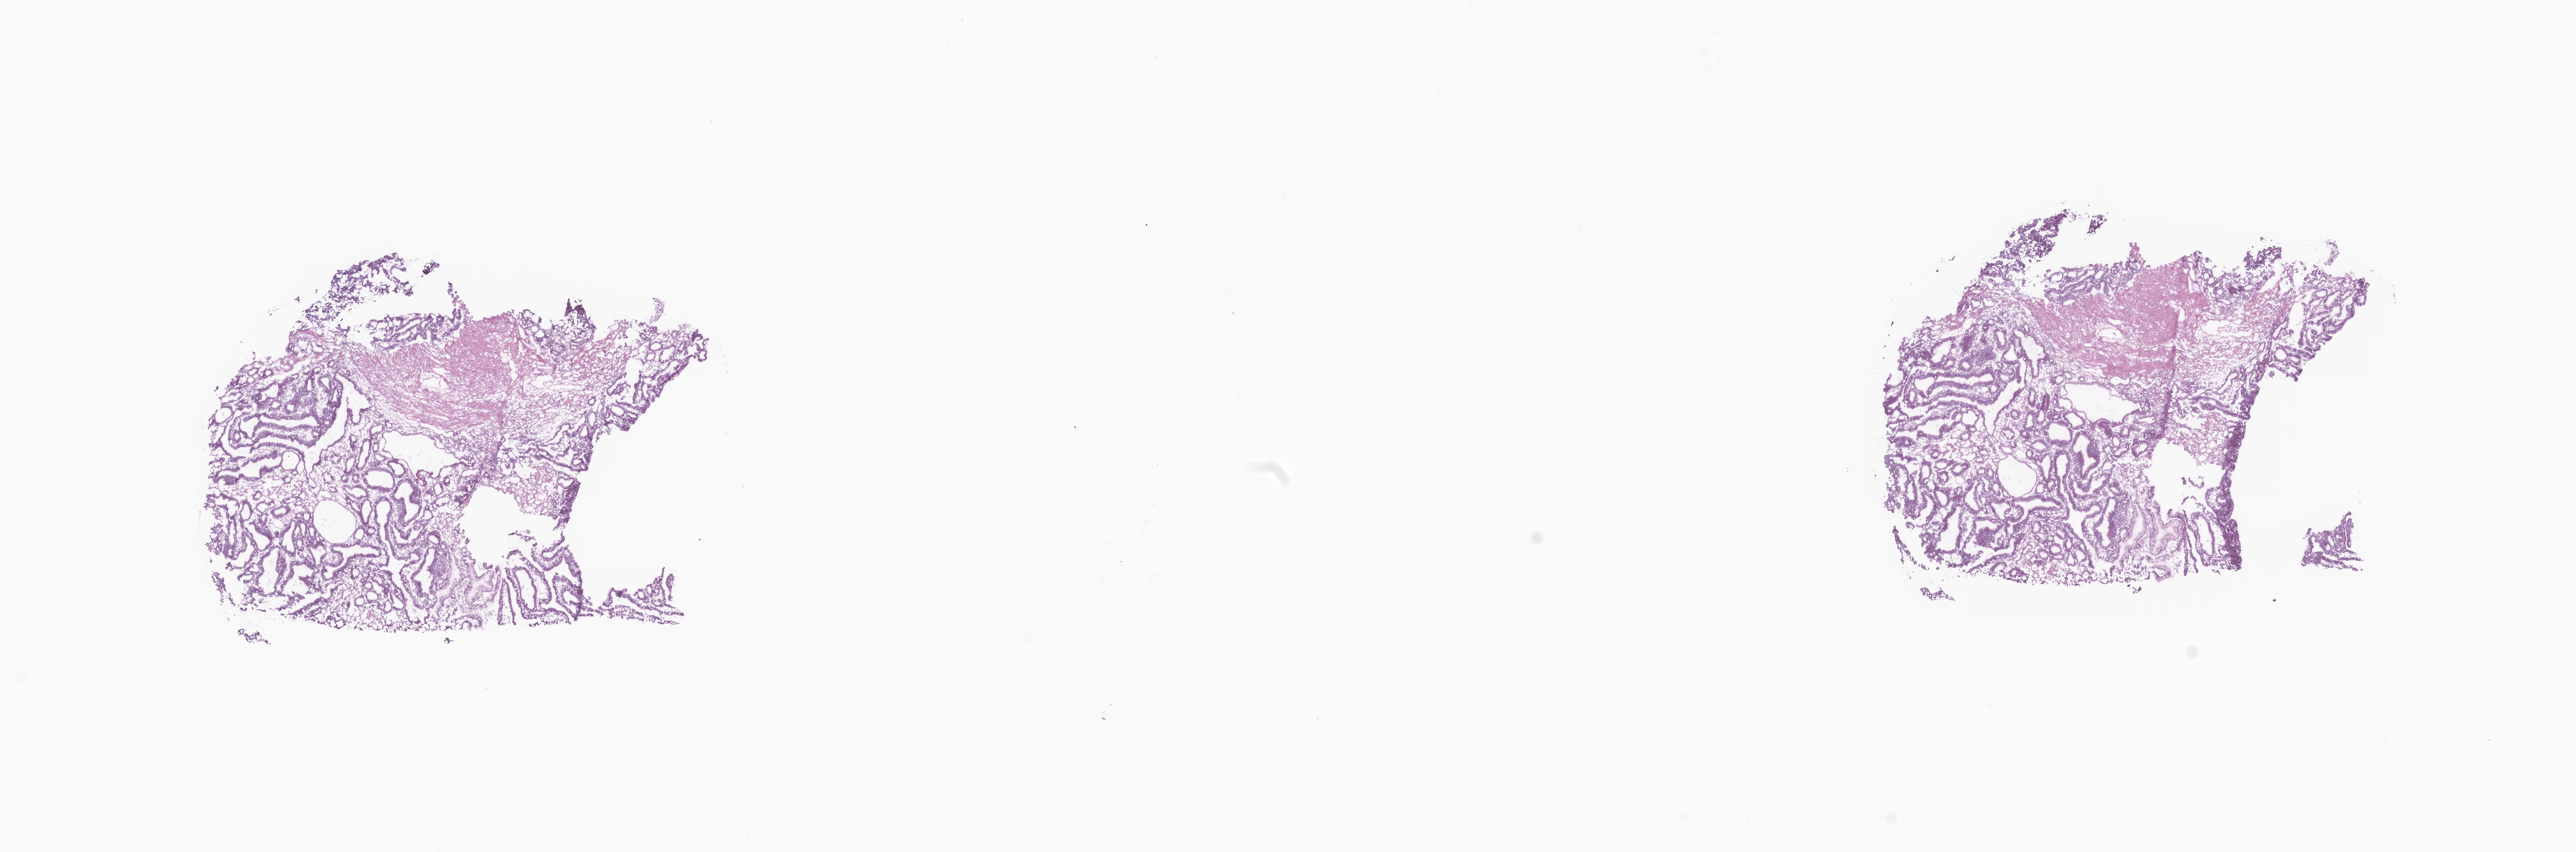
Whole-slide image, hematoxylin and eosin (H&E) stain, whole scanned area (about 23.2 x 7.7 mm) shown as a low-resolution overview; frozen section (tissue freezing medium); premalignant lesion from a patient with adenocarcinoma, NOS; anatomic site: ampulla of vater. Female patient; age at initial diagnosis 70 years. Composition of this section per pathologist review: tumor cells 0%, tumor nuclei 80%, stromal cells 90%, necrosis 0%, normal cells 10%. Infiltration values recorded for this section: lymphocyte infiltration 5%, monocyte infiltration 2%, neutrophil infiltration 5%.
This section: sample classed premalignant; the patient's recorded diagnosis is given above. Section: bottom of the tissue portion.